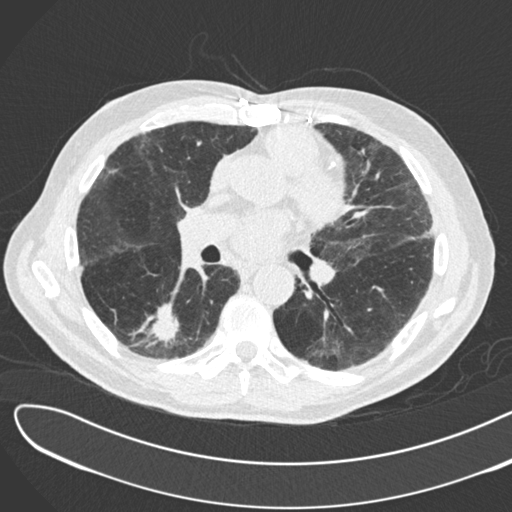
Low-dose screening chest CT, one axial slice. Slice 90 of 183 in the series (ordered by position). Lung window (W 1500 / L -600 HU). 512 × 512 image matrix, field of view 370 × 370 mm.
Annotated regions visible in this slice (expert manual segmentation):
- lesion 1 (tumor, lower lobe of right lung): bounding box (x1, y1, x2, y2) in pixels: (151, 301, 180, 345)